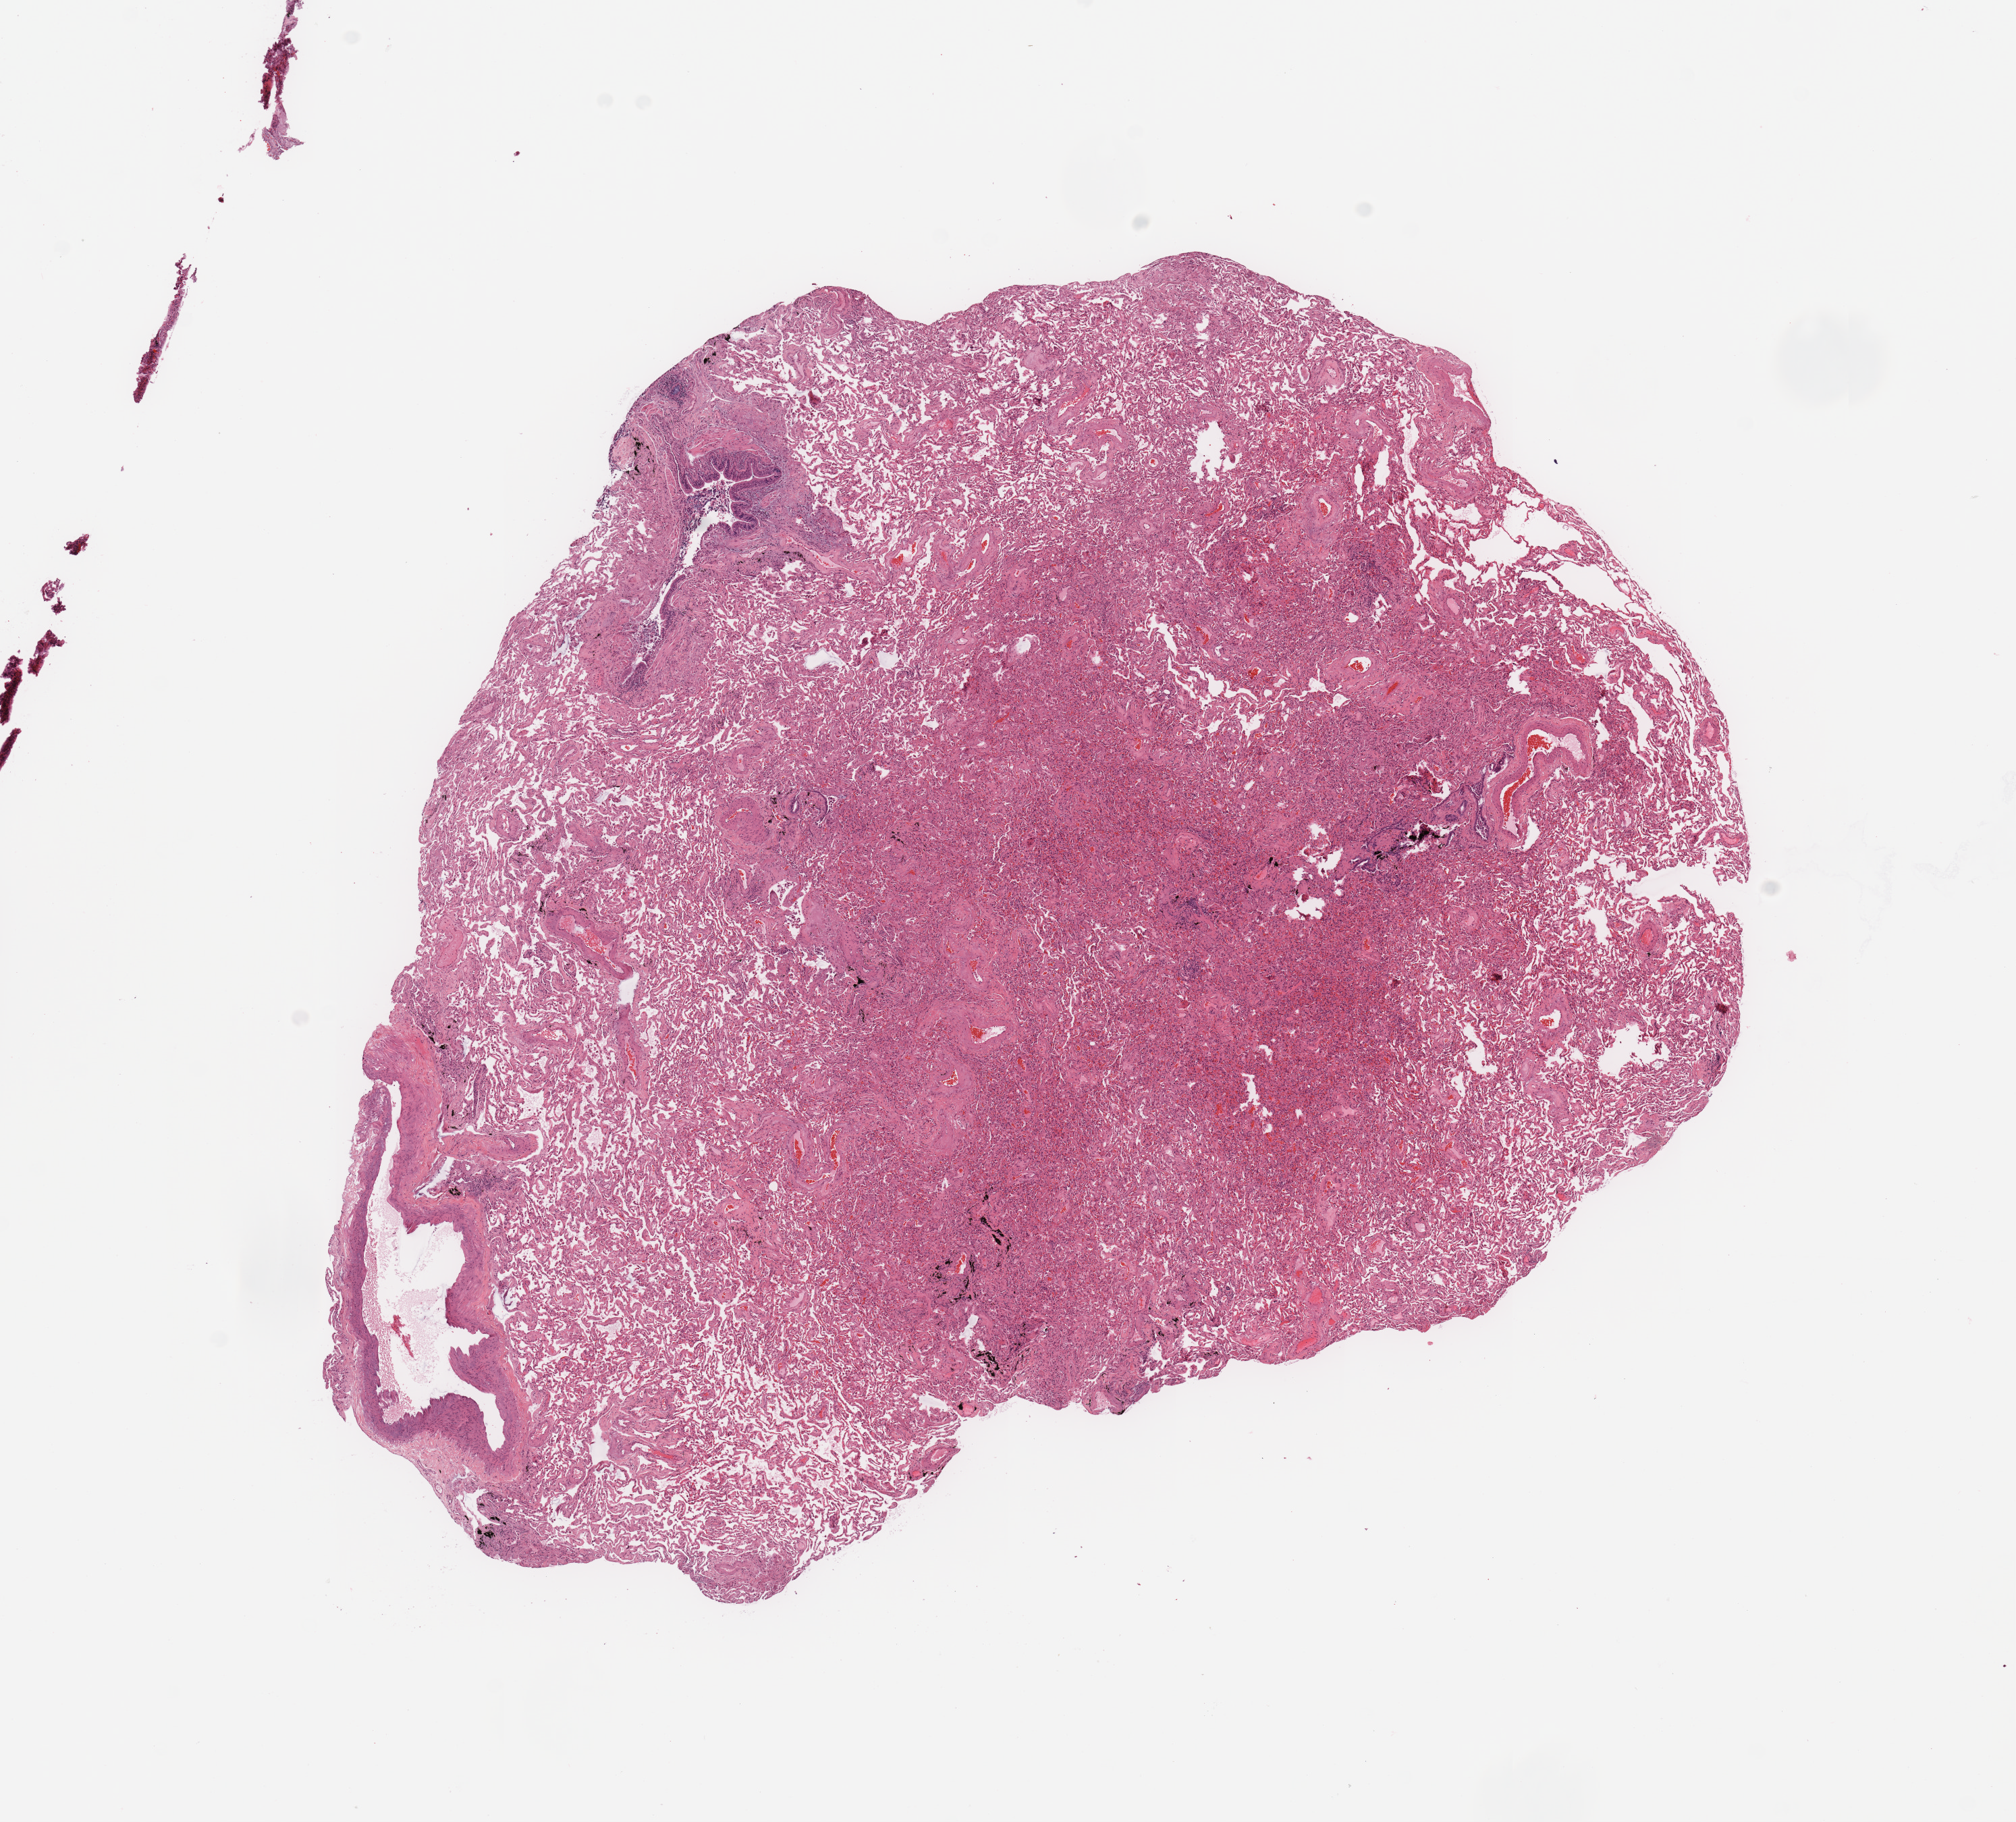
Digitized H&E tissue section (whole slide), a low-resolution overview of the entire scanned area, about 11.8 x 10.7 mm (from a 20x scan); lung, normal (non-tumour) tissue. Patient: female, age 78 years.
This section: normal (non-tumour) tissue from the same patient. Patient diagnosis: Adenocarcinoma, NOS.